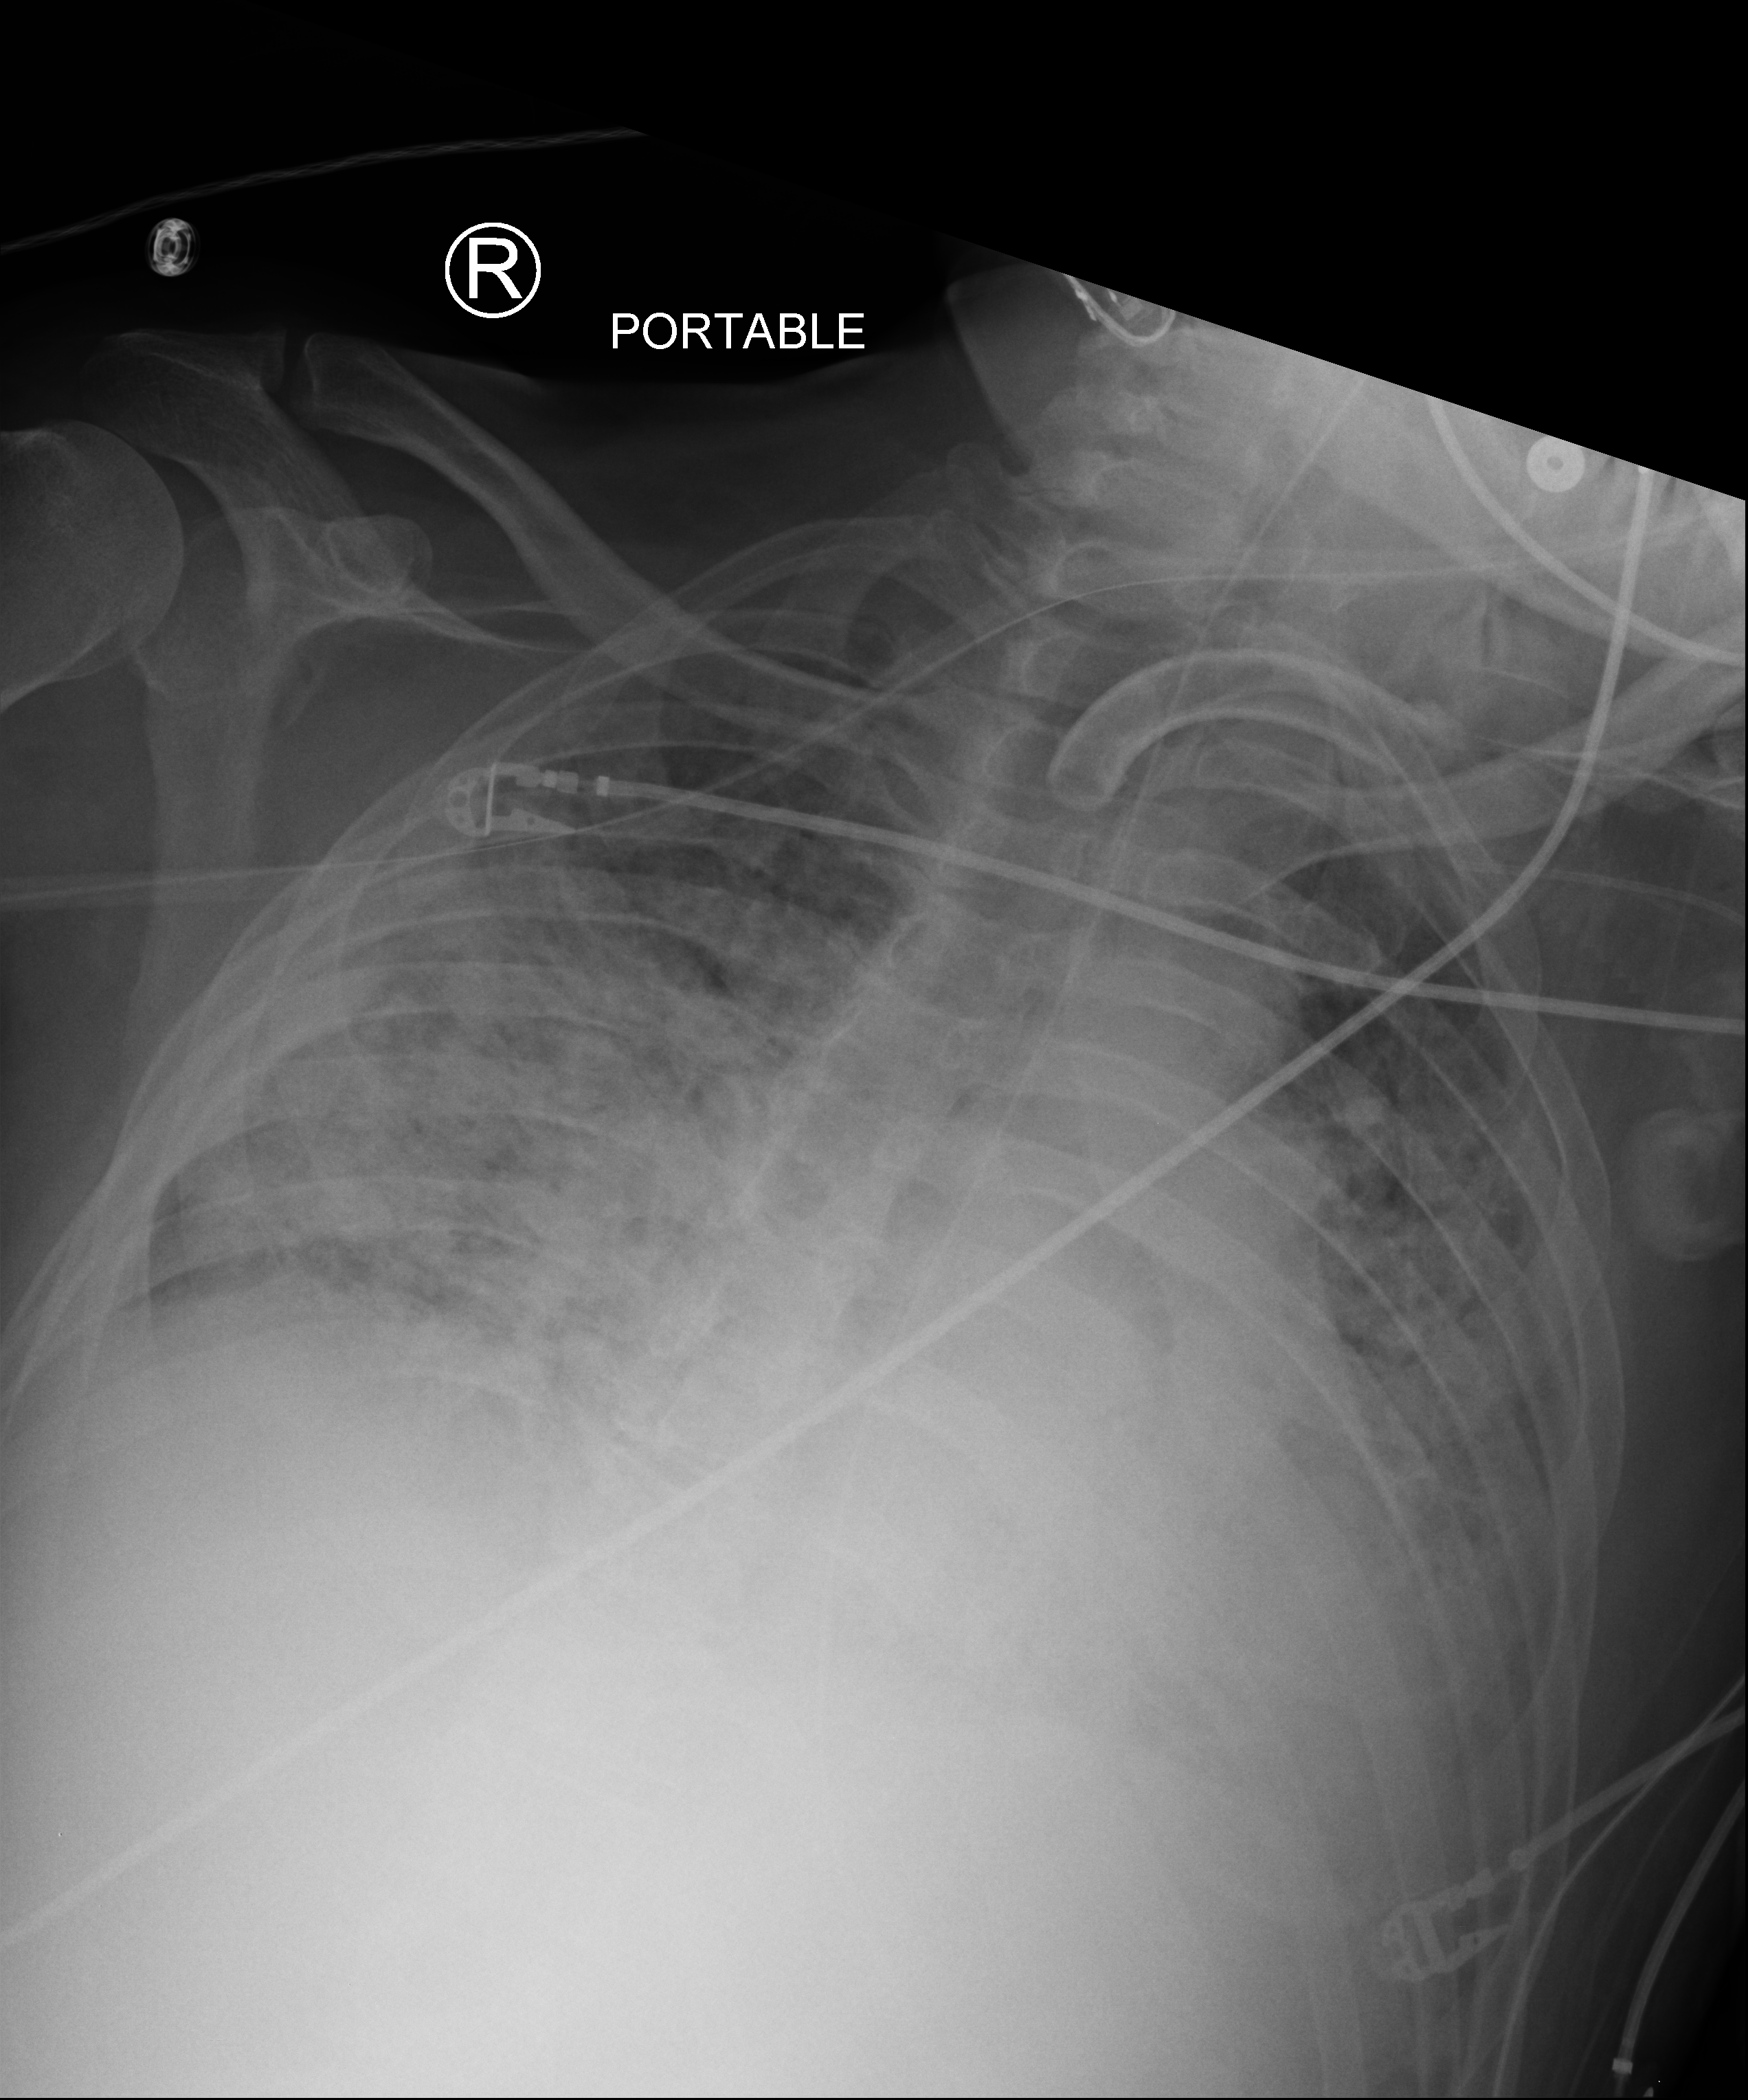
Chest X-ray (portable); anteroposterior (AP) projection. Patient hospitalised with COVID-19; male, aged 18–59 years.
Hospital-stay facts (about this admission, not read from this image; timing relative to this image not recorded): diabetes (admission record): no.